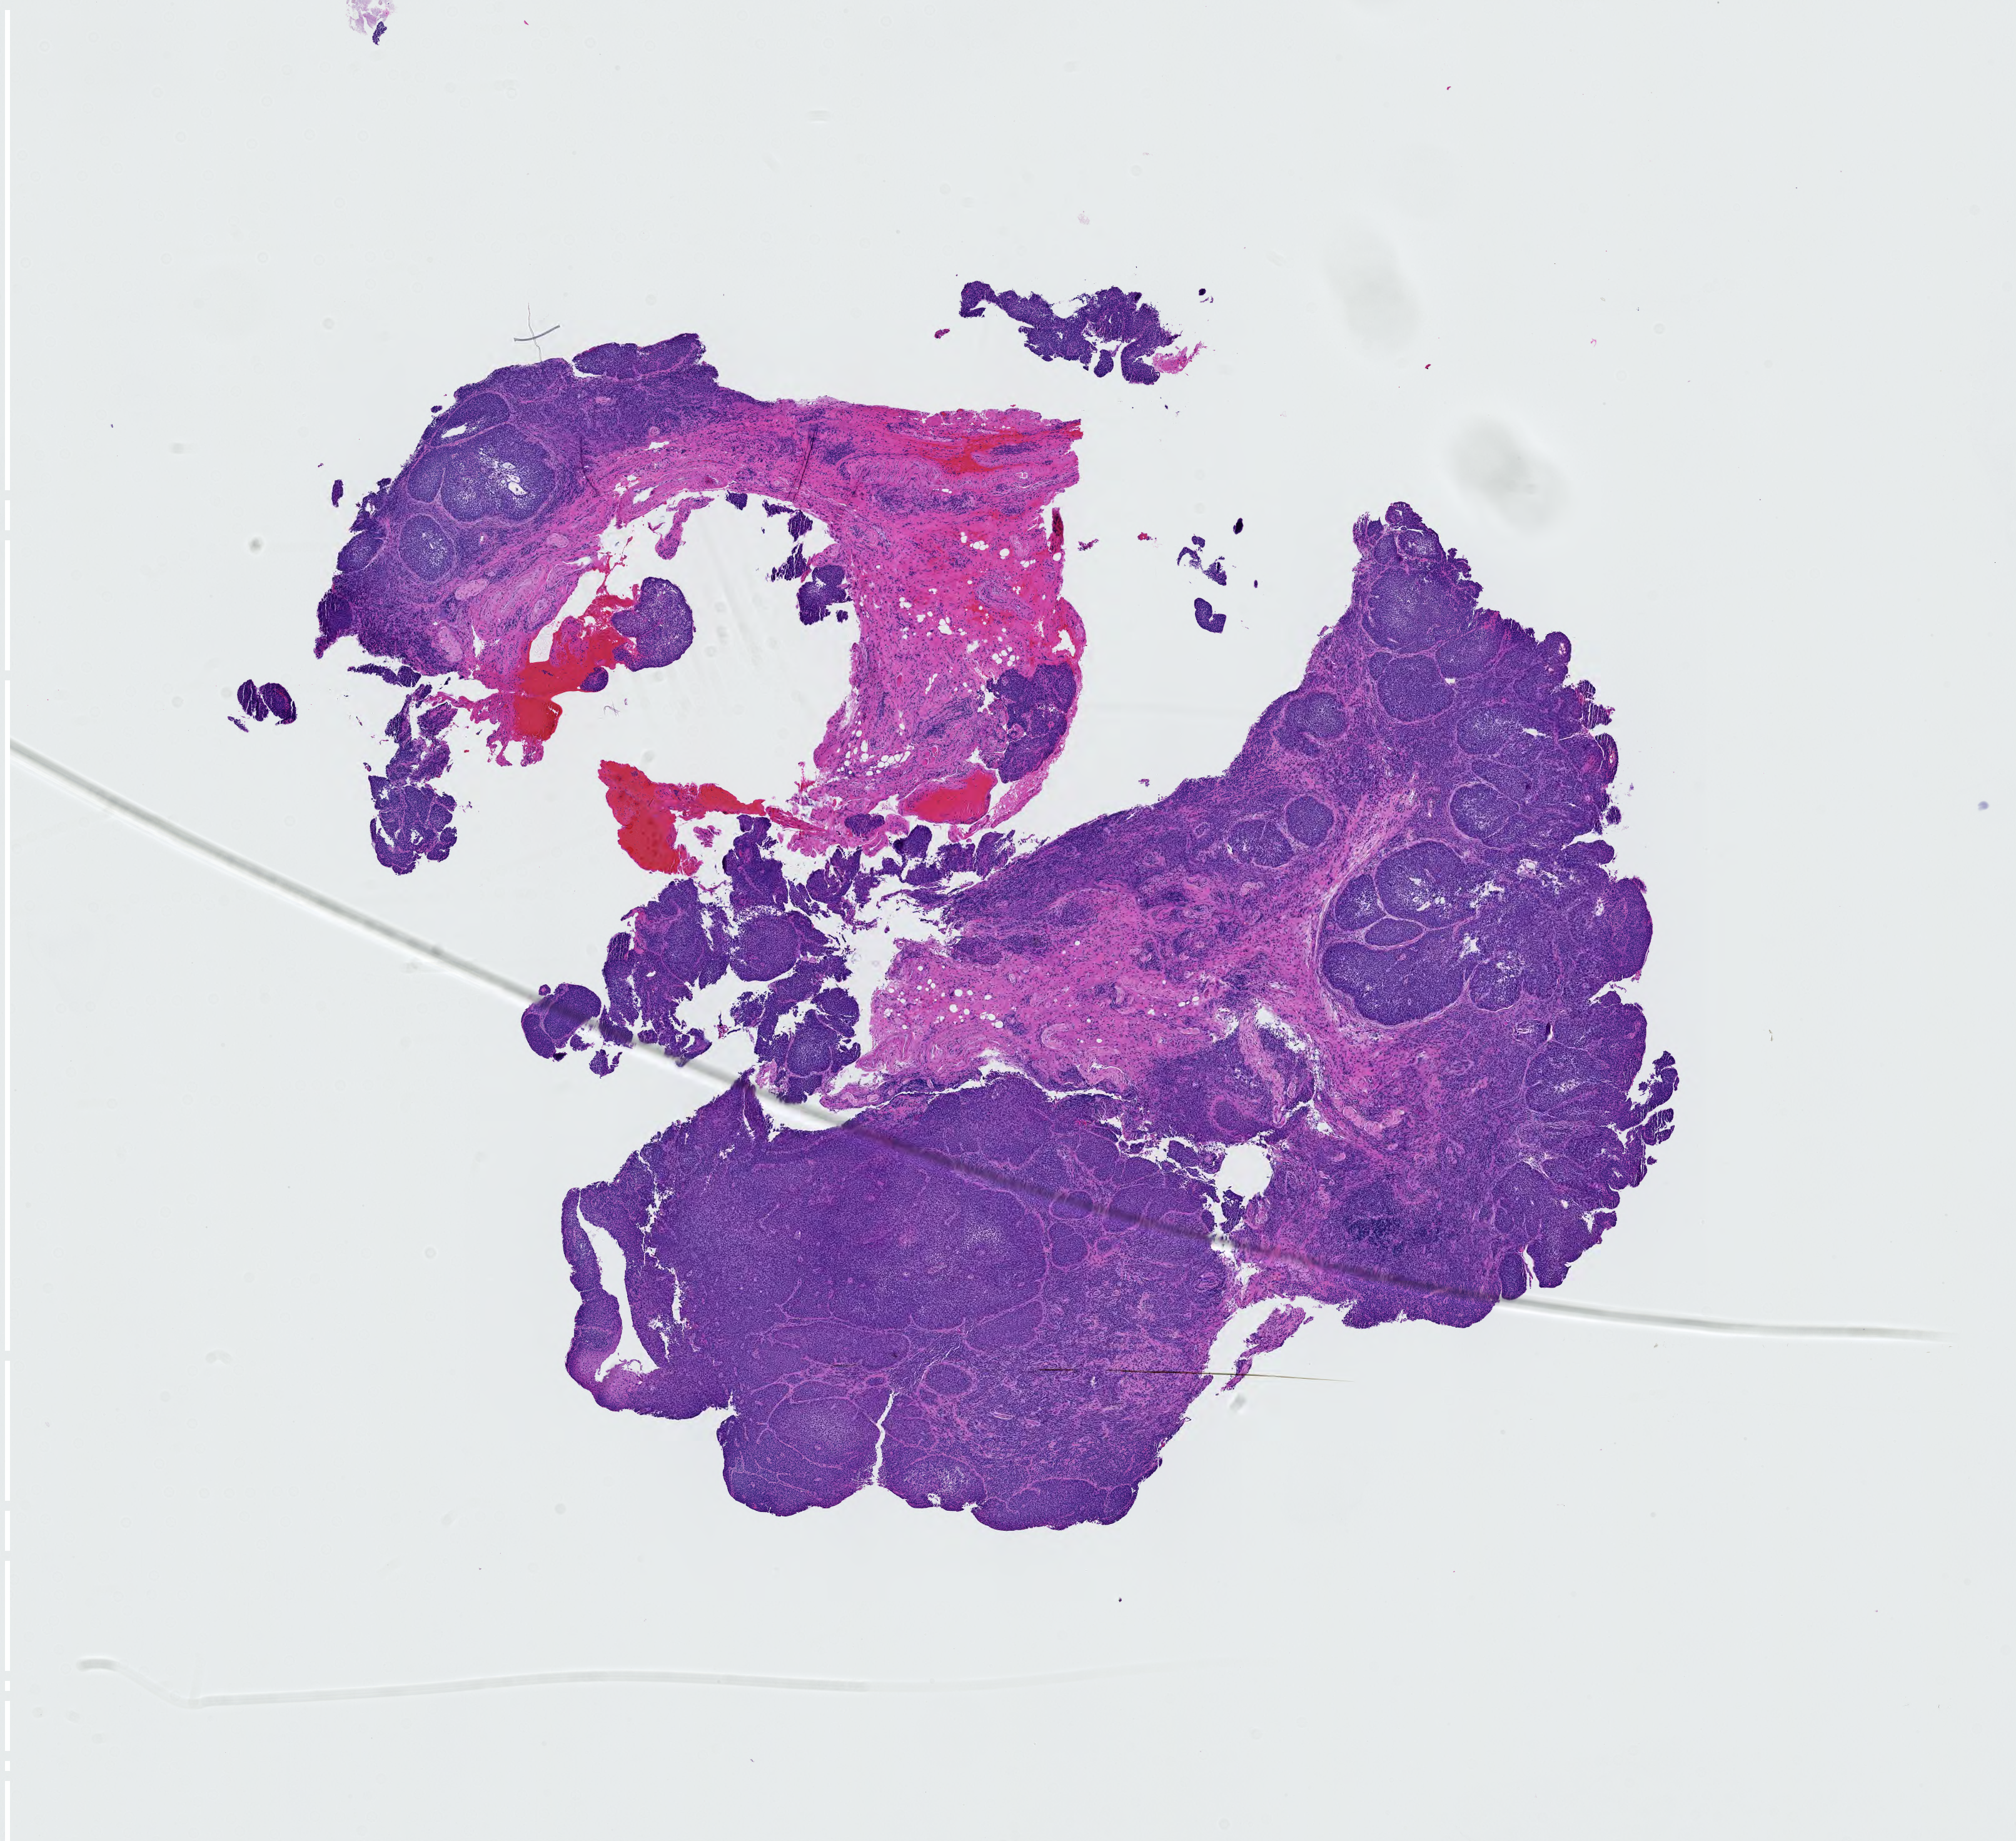
Digitized Hematoxylin and eosin (H&E) stained tissue section (whole slide) — shown as a low-resolution overview of the whole scanned area (about 11.7 x 10.7 mm, slide scanned at 40x), FFPE section, sample: primary tumour, head and neck. Male, age 69 years at initial diagnosis. Histologic grade: G3 (poorly differentiated).
TNM: T1 N0 M0. Histologic diagnosis: Basaloid squamous cell carcinoma (larynx, NOS). AJCC pathologic stage: I. Laterality: right.